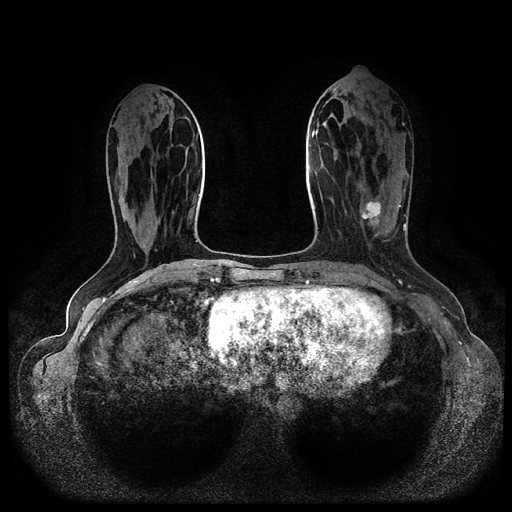
Breast MRI (dynamic contrast-enhanced, multi-phase), one axial slice; slice 37 of 116 in the series (ordered by position); dynamic contrast-enhanced series, time point 2 of 5 at this slice position (early post-contrast); 1.5 T; TE 2.6 ms, TR 5.3 ms; 2 mm slice thickness; 512 × 512 image matrix, field of view 350 × 350 mm. Female patient, age 45 years.
Structures marked on this image (semi-automatically segmented with operator editing):
- breast lesion (labelled 'tumour' in the annotation; benign lesions carry a separate 'benign' label): box from (x=355, y=197) to (x=387, y=228) px